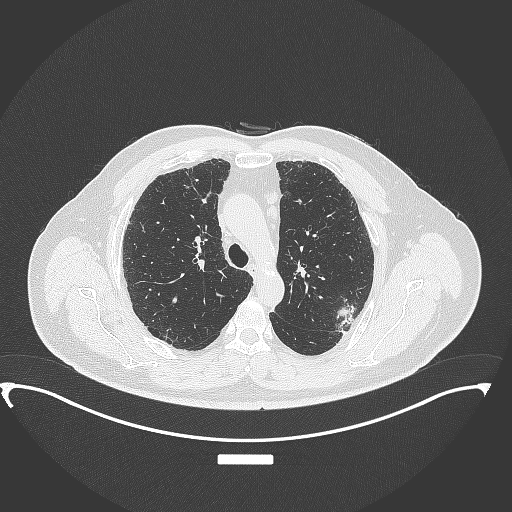
Chest CT, one axial slice; slice 256 of 350 in the series (ordered by position); lung window (W 1500 / L -600 HU); 1 mm slice thickness; 512 × 512 image matrix, field of view 459 × 459 mm. Male patient, age 64 years. Case-level facts recorded for this patient, not image findings: clinical TNM (as recorded): T1c N1 M1.
Outlined on this slice (bounding box drawn by a radiologist):
- lung tumour (recorded histology: adenocarcinoma): bounding box <334,297,363,338> (left, top, right, bottom; pixels)